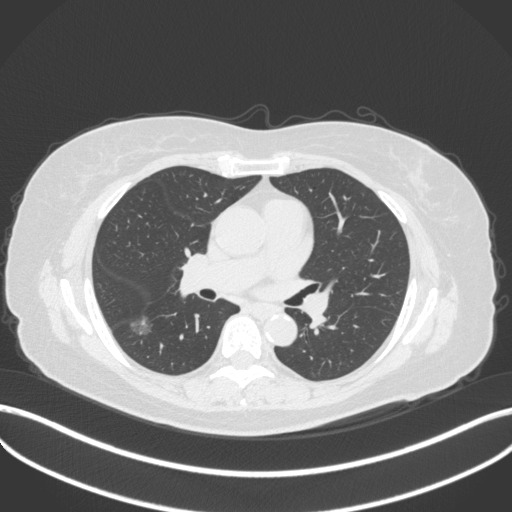
Chest CT, one axial slice; slice 176 of 322 in the series (ordered by position); reconstruction kernel B31f; lung window (W 1500 / L -600 HU); 1 mm slice thickness; 512 × 512 image matrix, field of view 400 × 400 mm. Patient: female, 64 years. Case-level facts recorded for this patient, not image findings: clinical TNM (as recorded): T1c N0 M0; histopathological grade: G1.
Structures marked on this image (rectangle marked by the reading radiologist):
- lung tumour (recorded histology: adenocarcinoma): box from (x=130, y=315) to (x=155, y=339) px